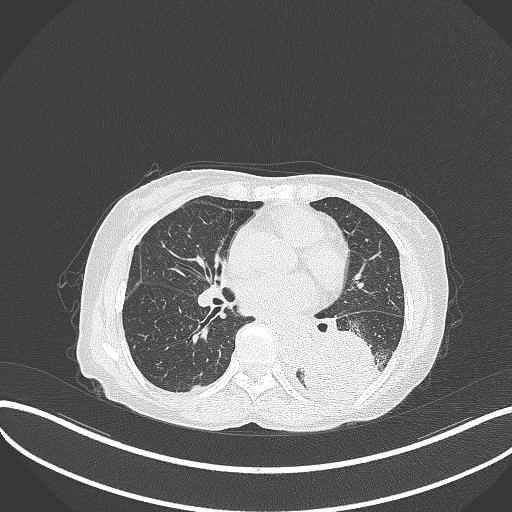
Chest CT, one axial slice; position 145 of 370 along the scan axis; reconstruction kernel B70f; 120 kVp; lung window (W 1500 / L -600 HU); 512 × 512 image matrix, field of view 400 × 400 mm. Female patient, age 78 years. From the clinical record (not read from this slice): clinical TNM (as recorded): T3 N0 M1.
Annotated regions visible in this slice (bounding box drawn by a radiologist):
- lung tumour (recorded histology: squamous cell carcinoma): box from (x=301, y=326) to (x=389, y=404) px